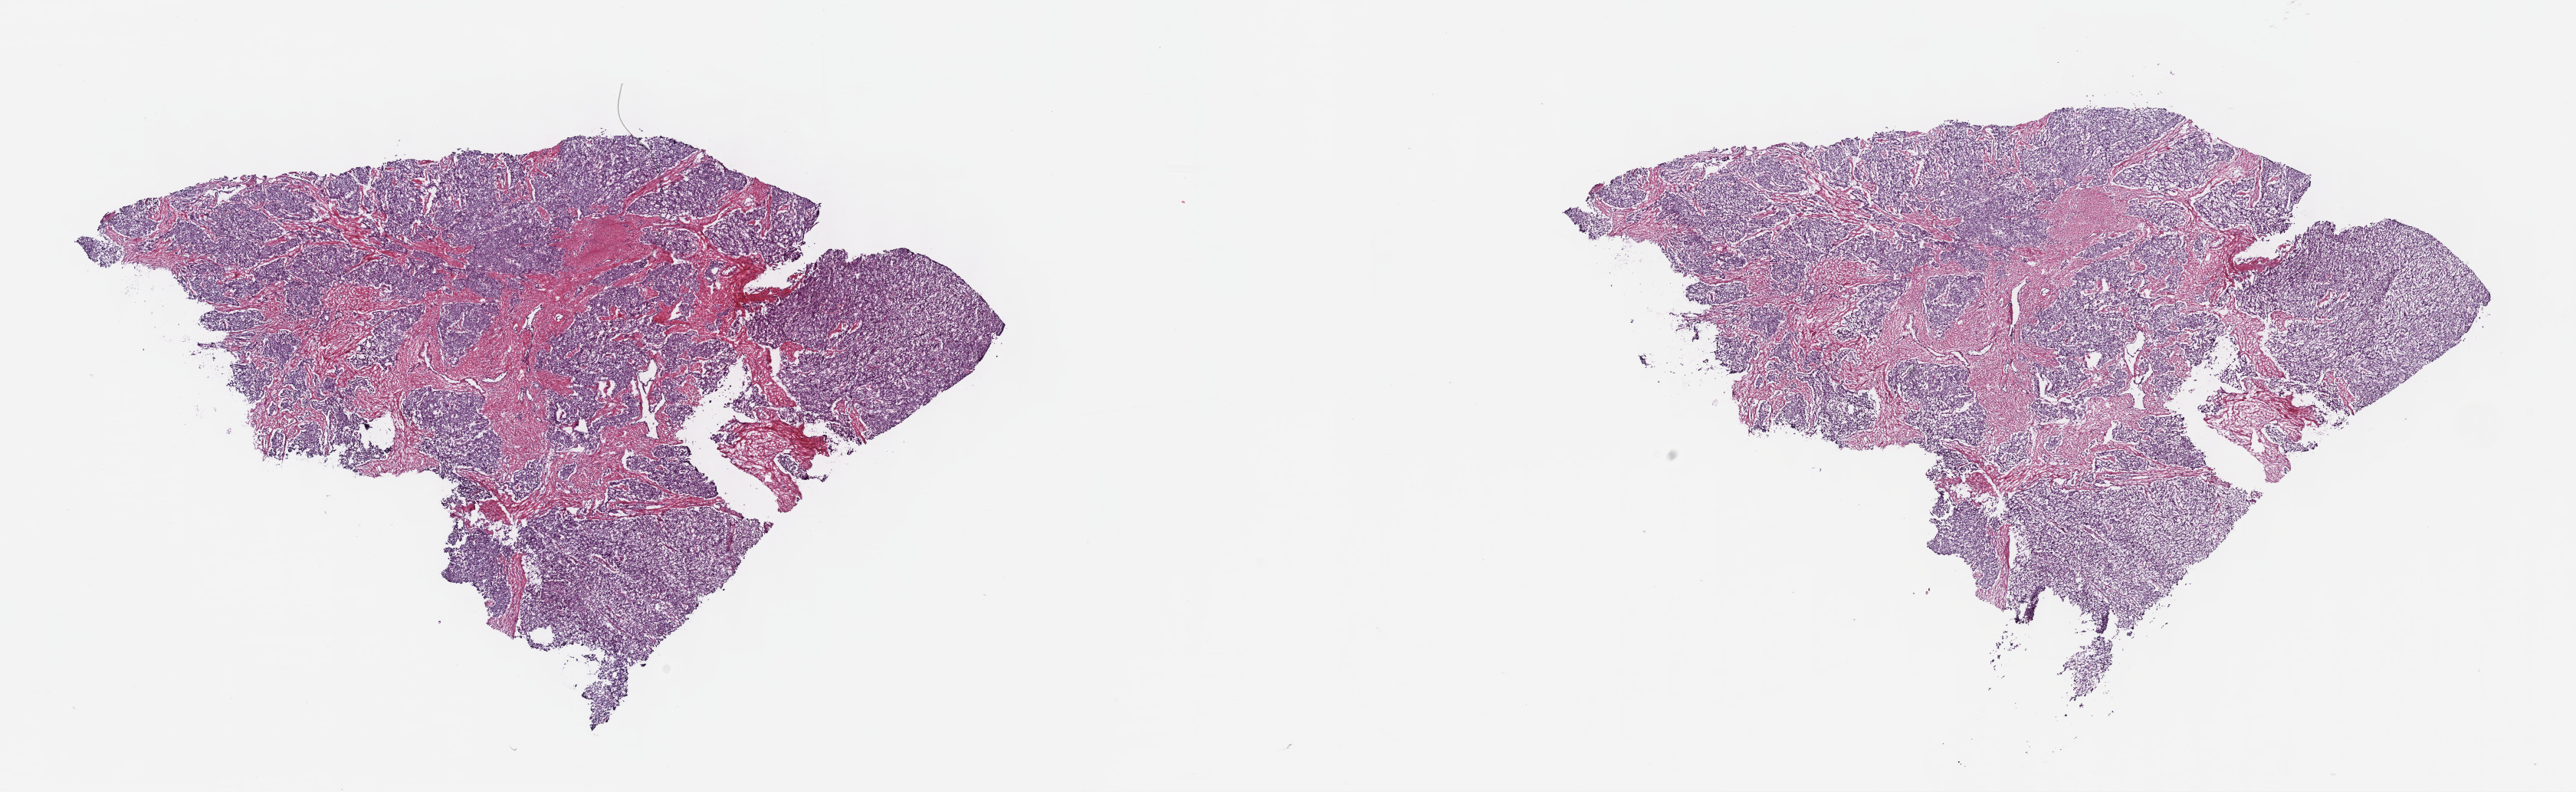
Whole-slide histology image, H&E — low-resolution overview of the scanned area, about 27.2 x 8.4 mm; frozen section from the top of the tissue portion; sample: primary tumour, prostate. Male, age 53 years at initial diagnosis. Gleason score: 8 (4+4). Pathologist review of this section (percent, as recorded): tumour cells 70%, tumour nuclei 85%, normal cells 5%, stromal cells 25%, necrosis 0%. Infiltration values recorded for this section: lymphocyte infiltration 0%, monocyte infiltration 0%, neutrophil infiltration 0%.
• laterality: bilateral
• lymph nodes positive (case pathology): 0 of 34 examined
• histologic diagnosis: Adenocarcinoma, NOS